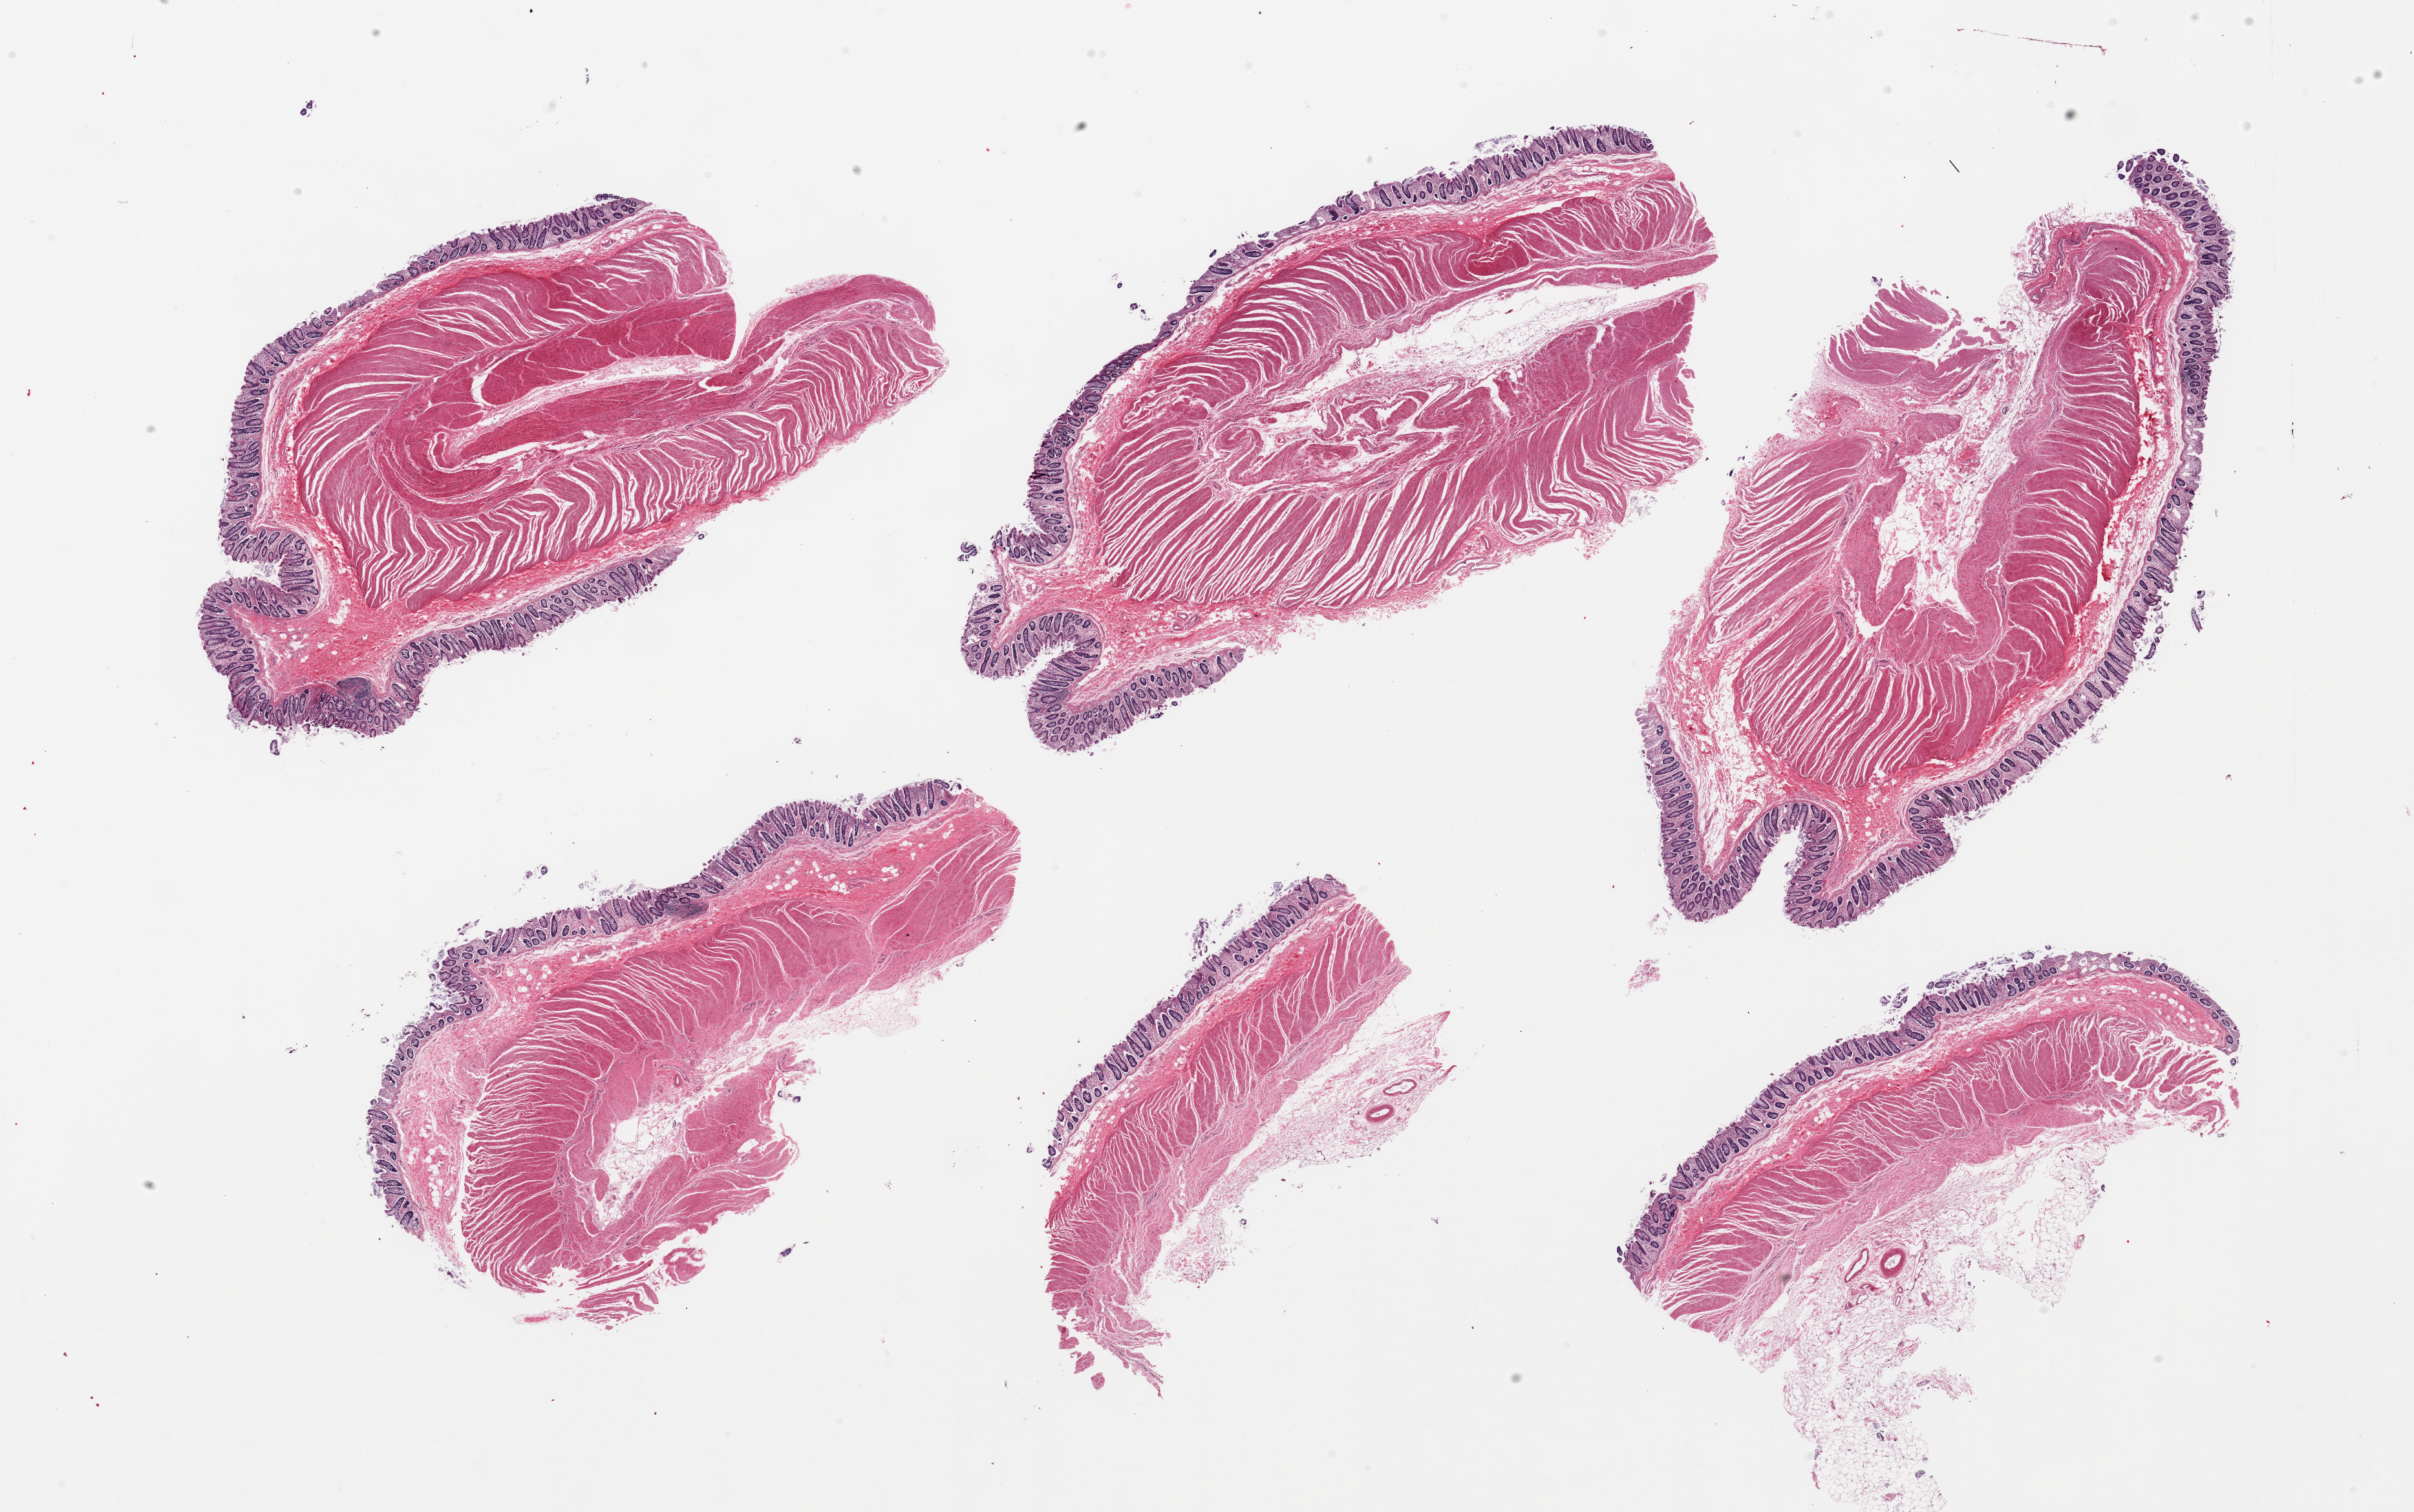
H&E whole-slide image — low-resolution overview of the scanned area, about 29.5 x 18.5 mm. Male donor.
* specimen: PAXgene-fixed, paraffin-embedded tissue; sampled site (target tissue): sigmoid colon; donor tissue sample